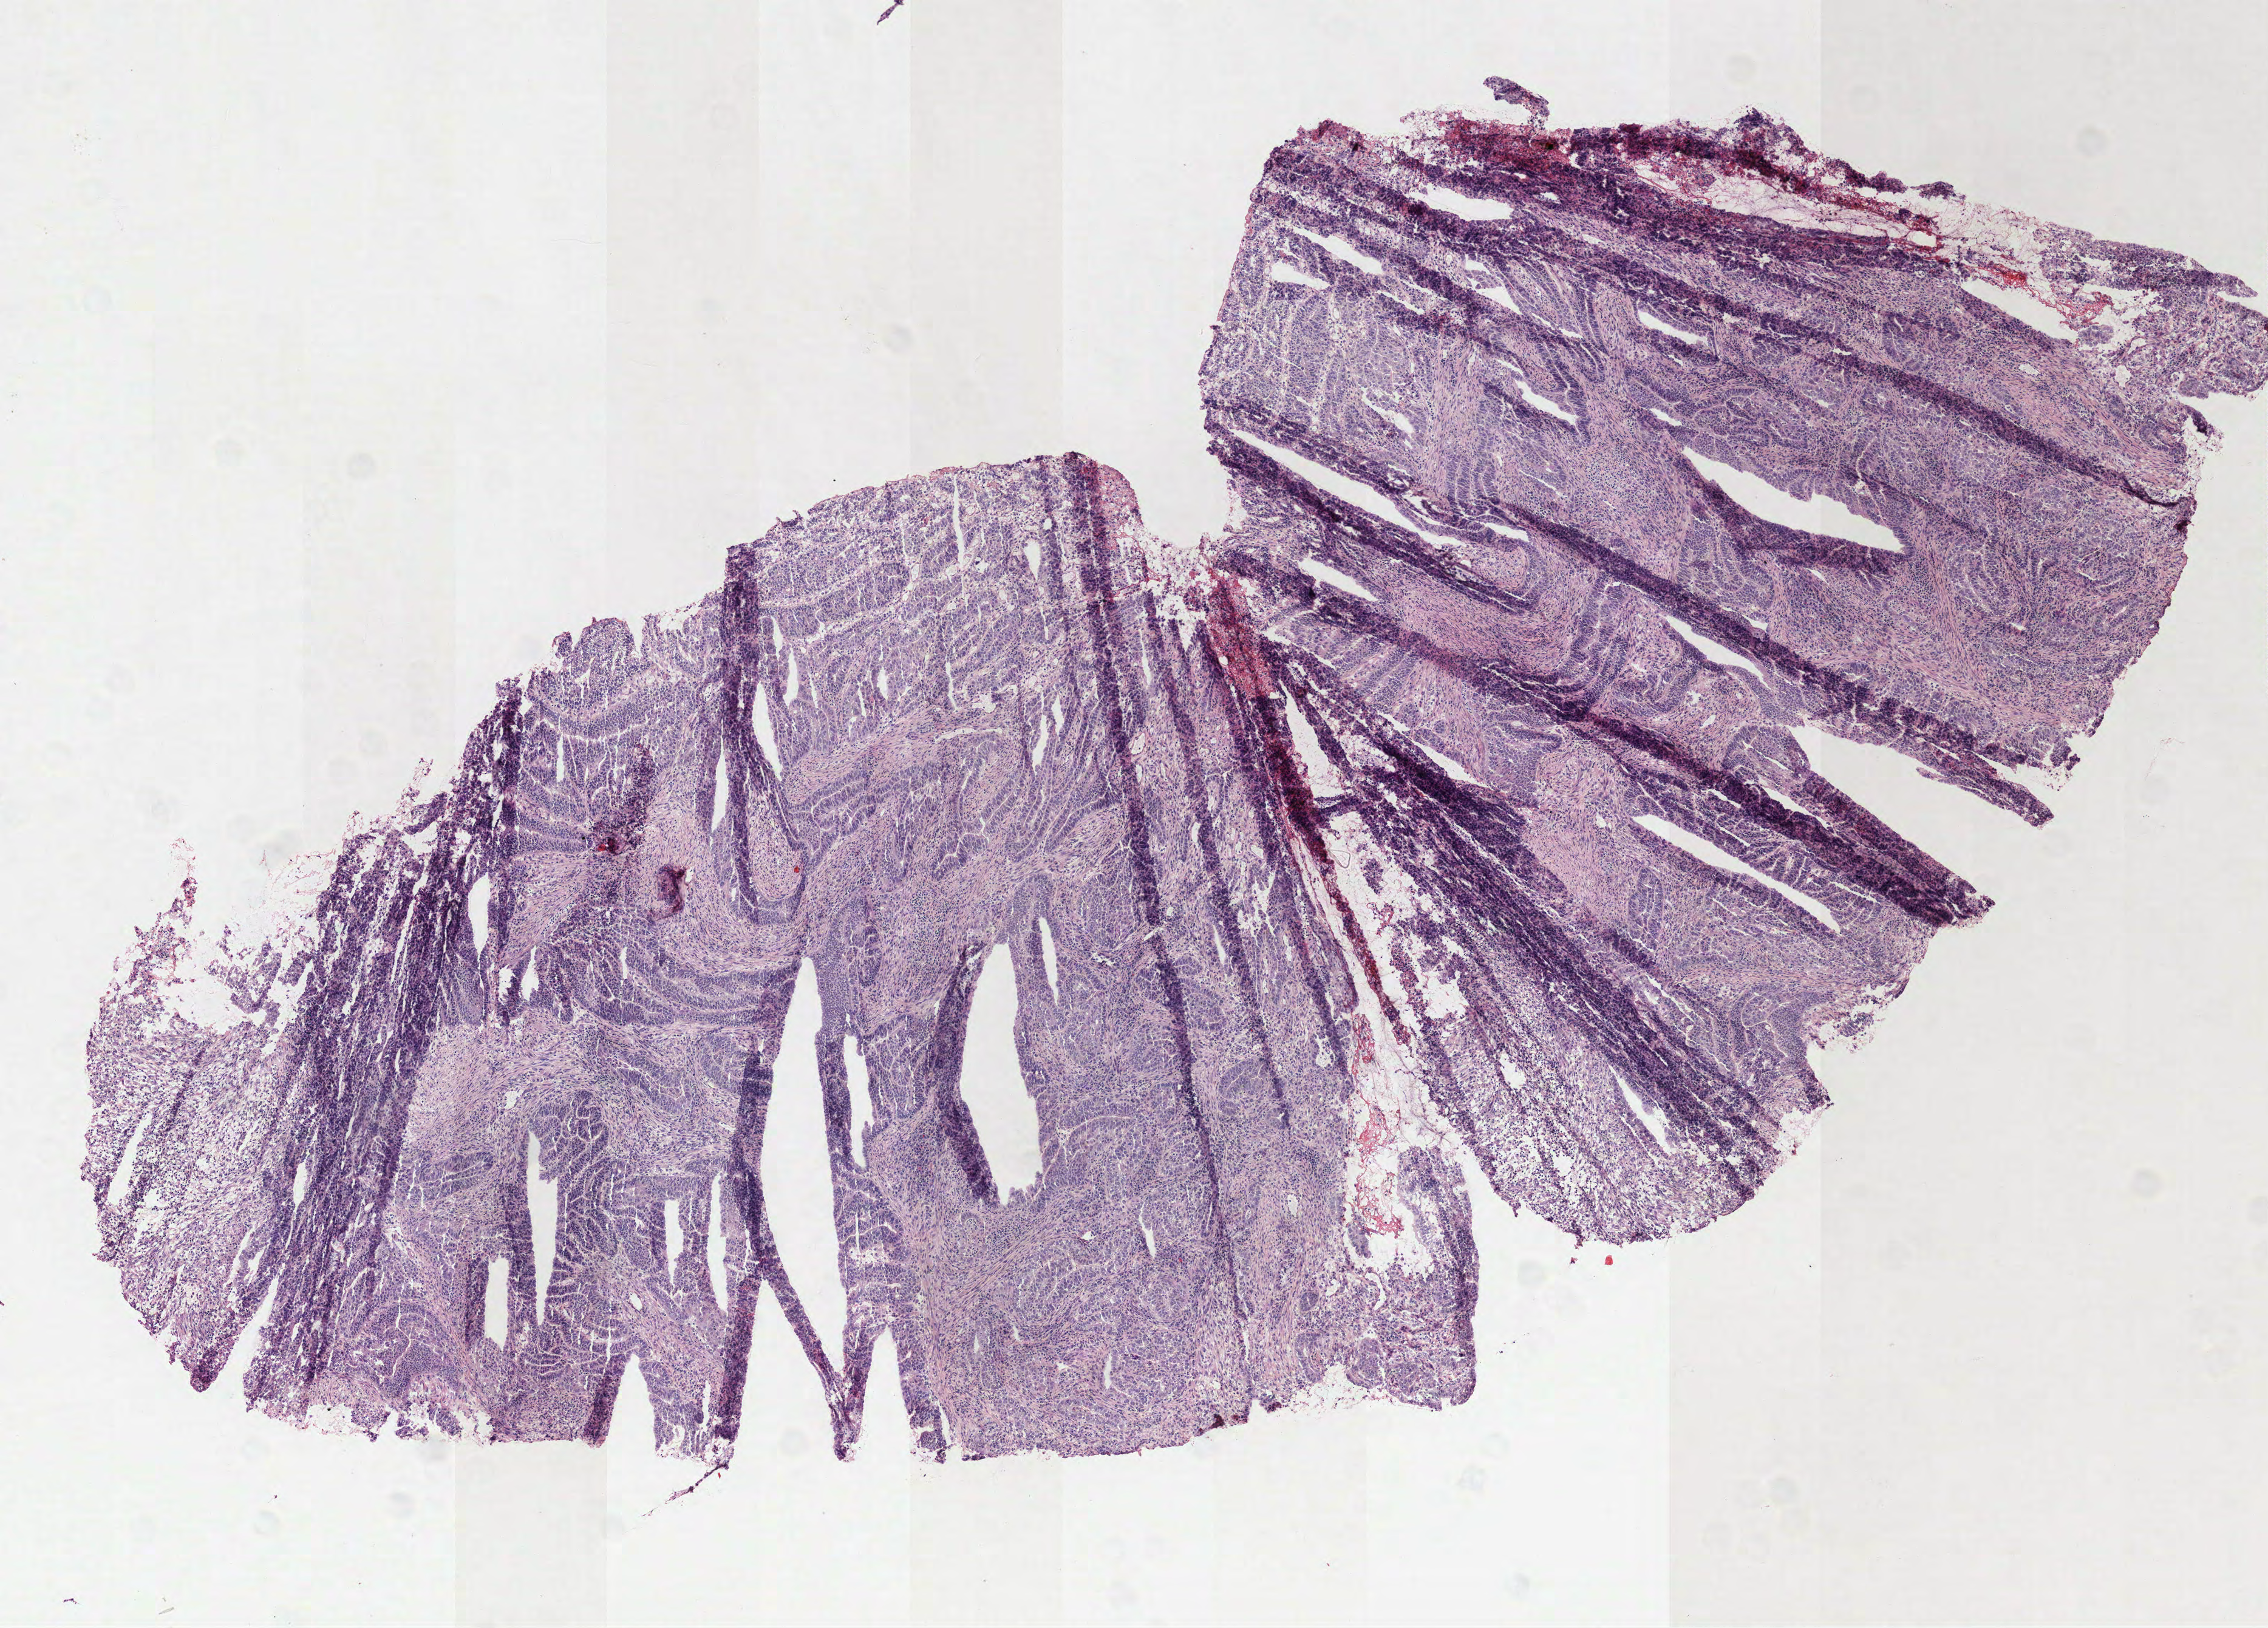
Hematoxylin and eosin (H&E) stained whole-slide image, low-resolution overview of the scanned area, about 7.5 x 5.4 mm (acquisition: 40x scan). Frozen section from the top of the tissue portion. Primary tumour sample from the stomach. Male patient; age at initial diagnosis 57 years. Histologic grade: G2 (moderately differentiated). Composition of this section per pathologist review: tumour cells 90%, tumour nuclei 75%, normal cells 0%, stromal cells 5%, necrosis 5%. Infiltration values recorded for this section: lymphocyte infiltration 20%, monocyte infiltration 0%, neutrophil infiltration 0%.
AJCC pathologic stage: IIB (7th edition). TNM: T2 N2 M0. Pathologic diagnosis: Adenocarcinoma, NOS (fundus of stomach).